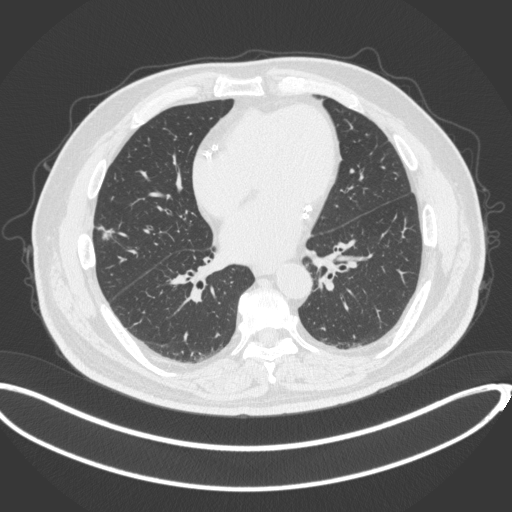
Chest CT, one axial slice. Position 140 of 342 along the scan axis. 120 kVp. Lung window (W 1500 / L -600 HU). 512 × 512 image matrix. Patient: male, 68 years. Case-level facts recorded for this patient, not image findings: clinical TNM (as recorded): T1c N0 M0.
Structures marked on this image (bounding box drawn by a radiologist):
- lung tumour (recorded histology: adenocarcinoma): bounding box <95,223,115,241> (left, top, right, bottom; pixels)